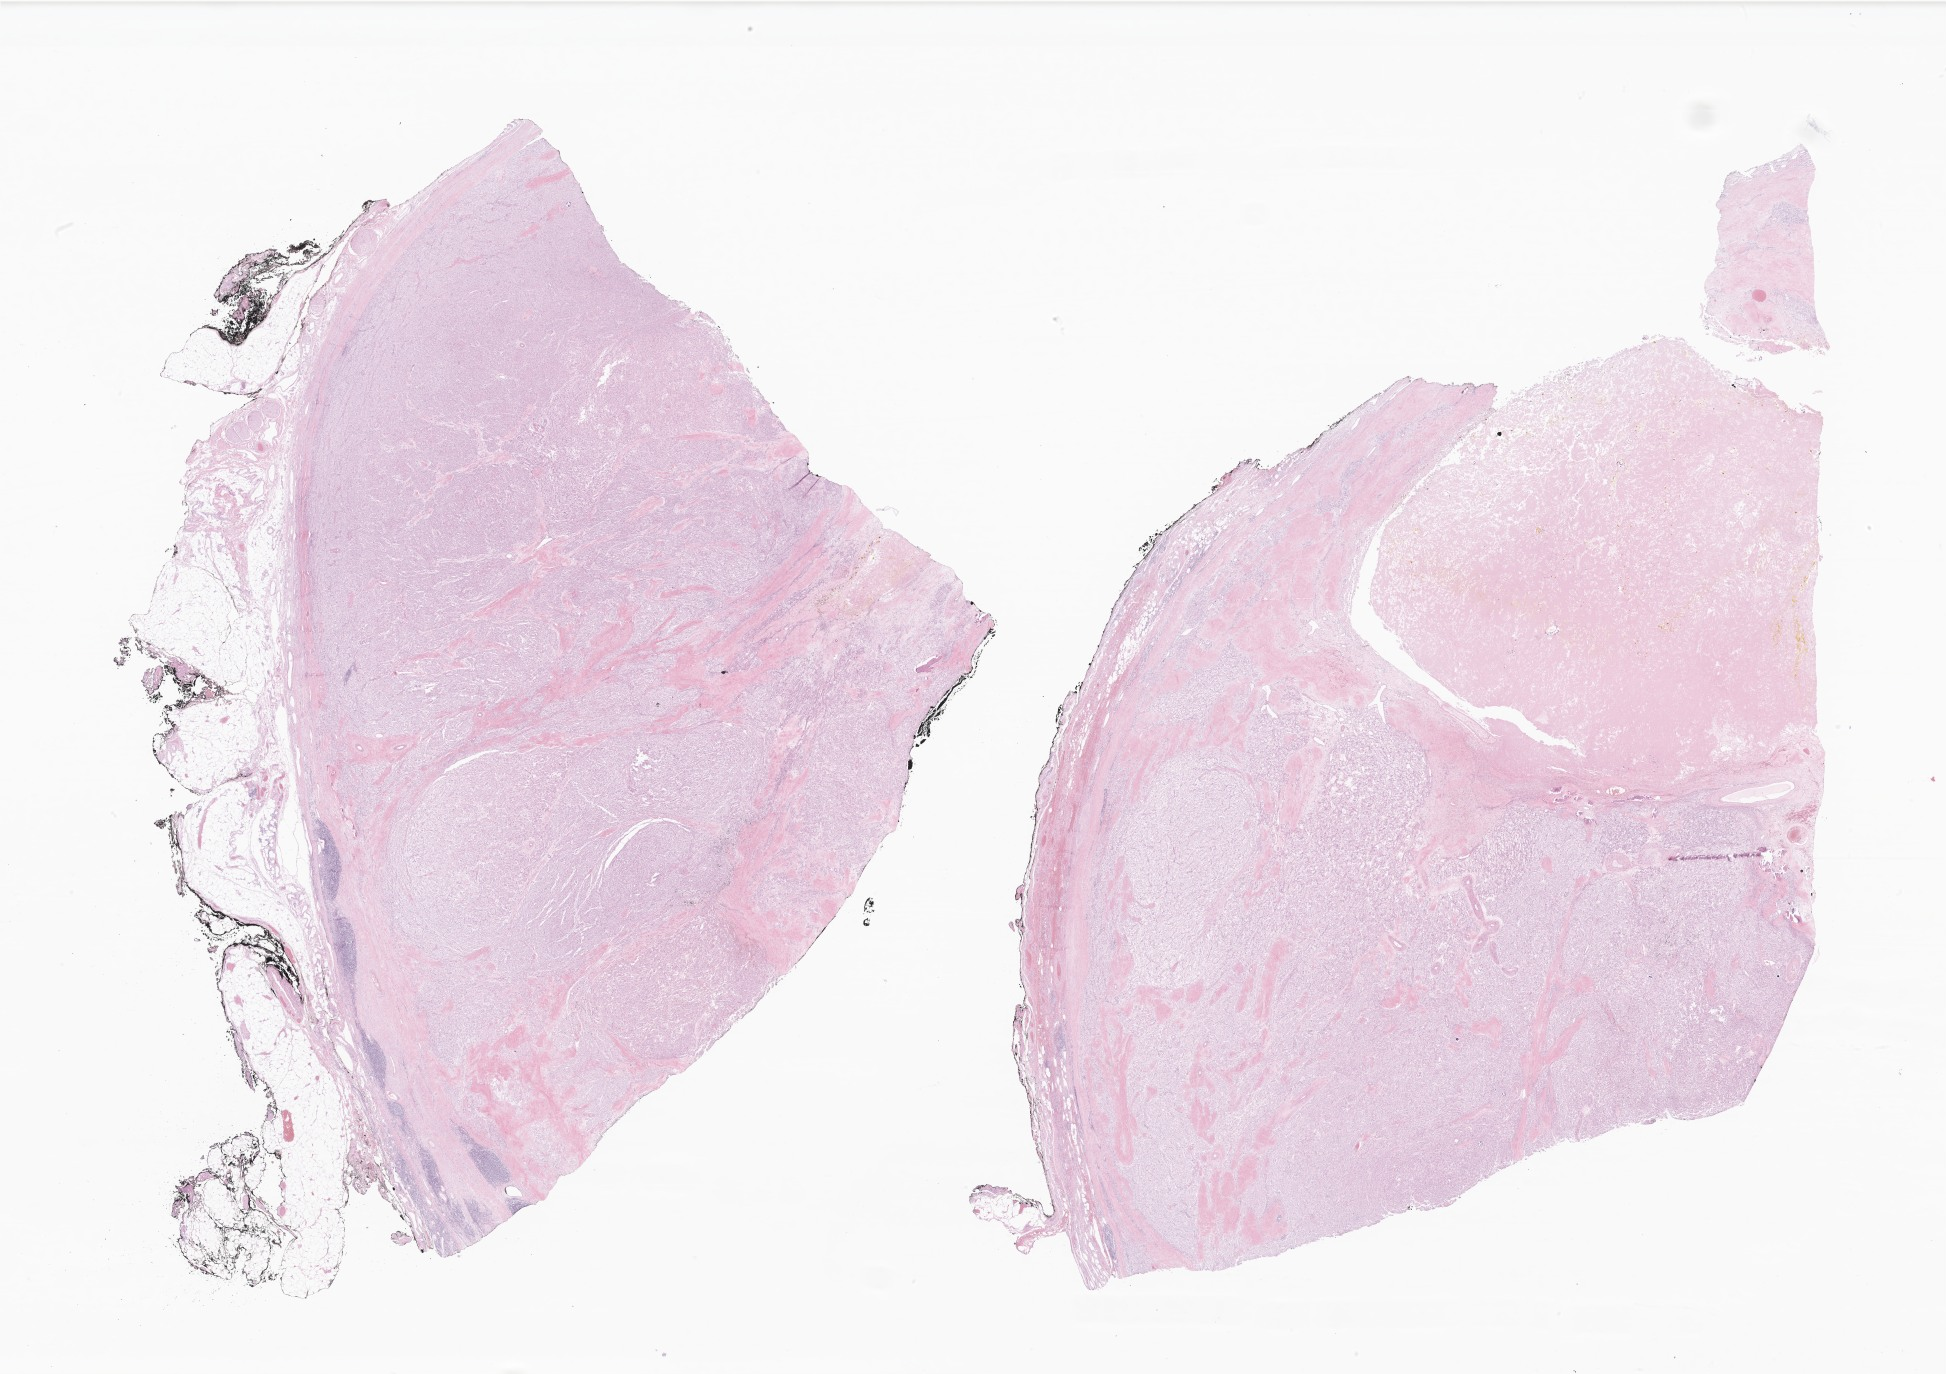
Whole-slide image, hematoxylin and eosin (H&E) stain of tumor tissue from the retroperitoneum, a low-resolution overview of the entire scanned area, about 32.8 x 23.2 mm. FFPE section. Patient female; age 204 months (17 years).
Recorded diagnosis: Alveolar soft part sarcoma.